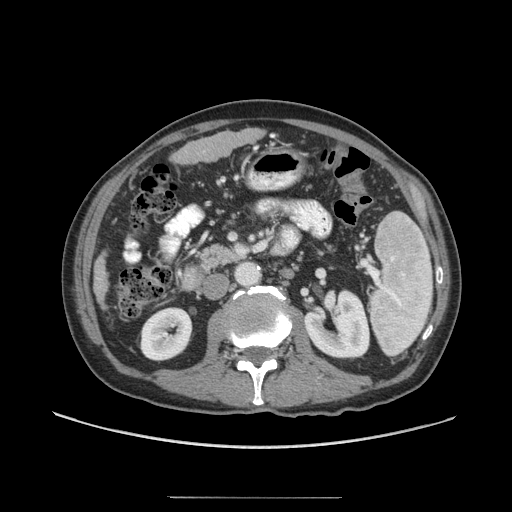
Contrast-enhanced abdominal CT (liver protocol), one axial slice. Slice 13 of 71 in the series (ordered by position). Reconstruction kernel STANDARD. Soft-tissue window (W 400 / L 40 HU). 2.5 mm slice thickness. 512 × 512 image matrix, field of view 400 × 400 mm. From the clinical record (not read from this slice): diagnosis: hepatocellular carcinoma (patient treated with transarterial chemoembolisation; whether this scan precedes or follows treatment is not stated here); TNM stage (as recorded): Stage-I; Child-Pugh class: A; tumour nodularity: uninodular; tumour size: 3.5 cm.
Outlined on this slice (semi-automatically segmented with operator editing):
- liver parenchyma outside the tumour (the mass and vessels are separate outlines, so this box may not span the whole liver): bounding box (x1, y1, x2, y2) in pixels: (94, 128, 261, 307)